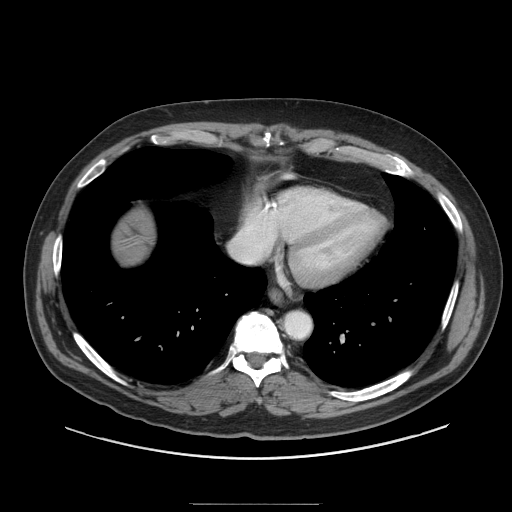
Contrast-enhanced abdominal CT (liver protocol), one axial slice; position 86 of 91 along the scan axis; reconstruction kernel STANDARD; soft-tissue window (W 400 / L 40 HU); 512 × 512 image matrix, field of view 440 × 440 mm. Case-level facts recorded for this patient, not image findings: diagnosis: hepatocellular carcinoma (patient treated with transarterial chemoembolisation; whether this scan precedes or follows treatment is not stated here); TNM stage (as recorded): Stage-I; Child-Pugh class: A; tumour nodularity: uninodular; tumour size: 4 cm.
Outlined on this slice (semi-automatically segmented with operator editing):
- liver parenchyma outside the tumour (the mass and vessels are separate outlines, so this box may not span the whole liver): box from (x=114, y=212) to (x=154, y=264) px